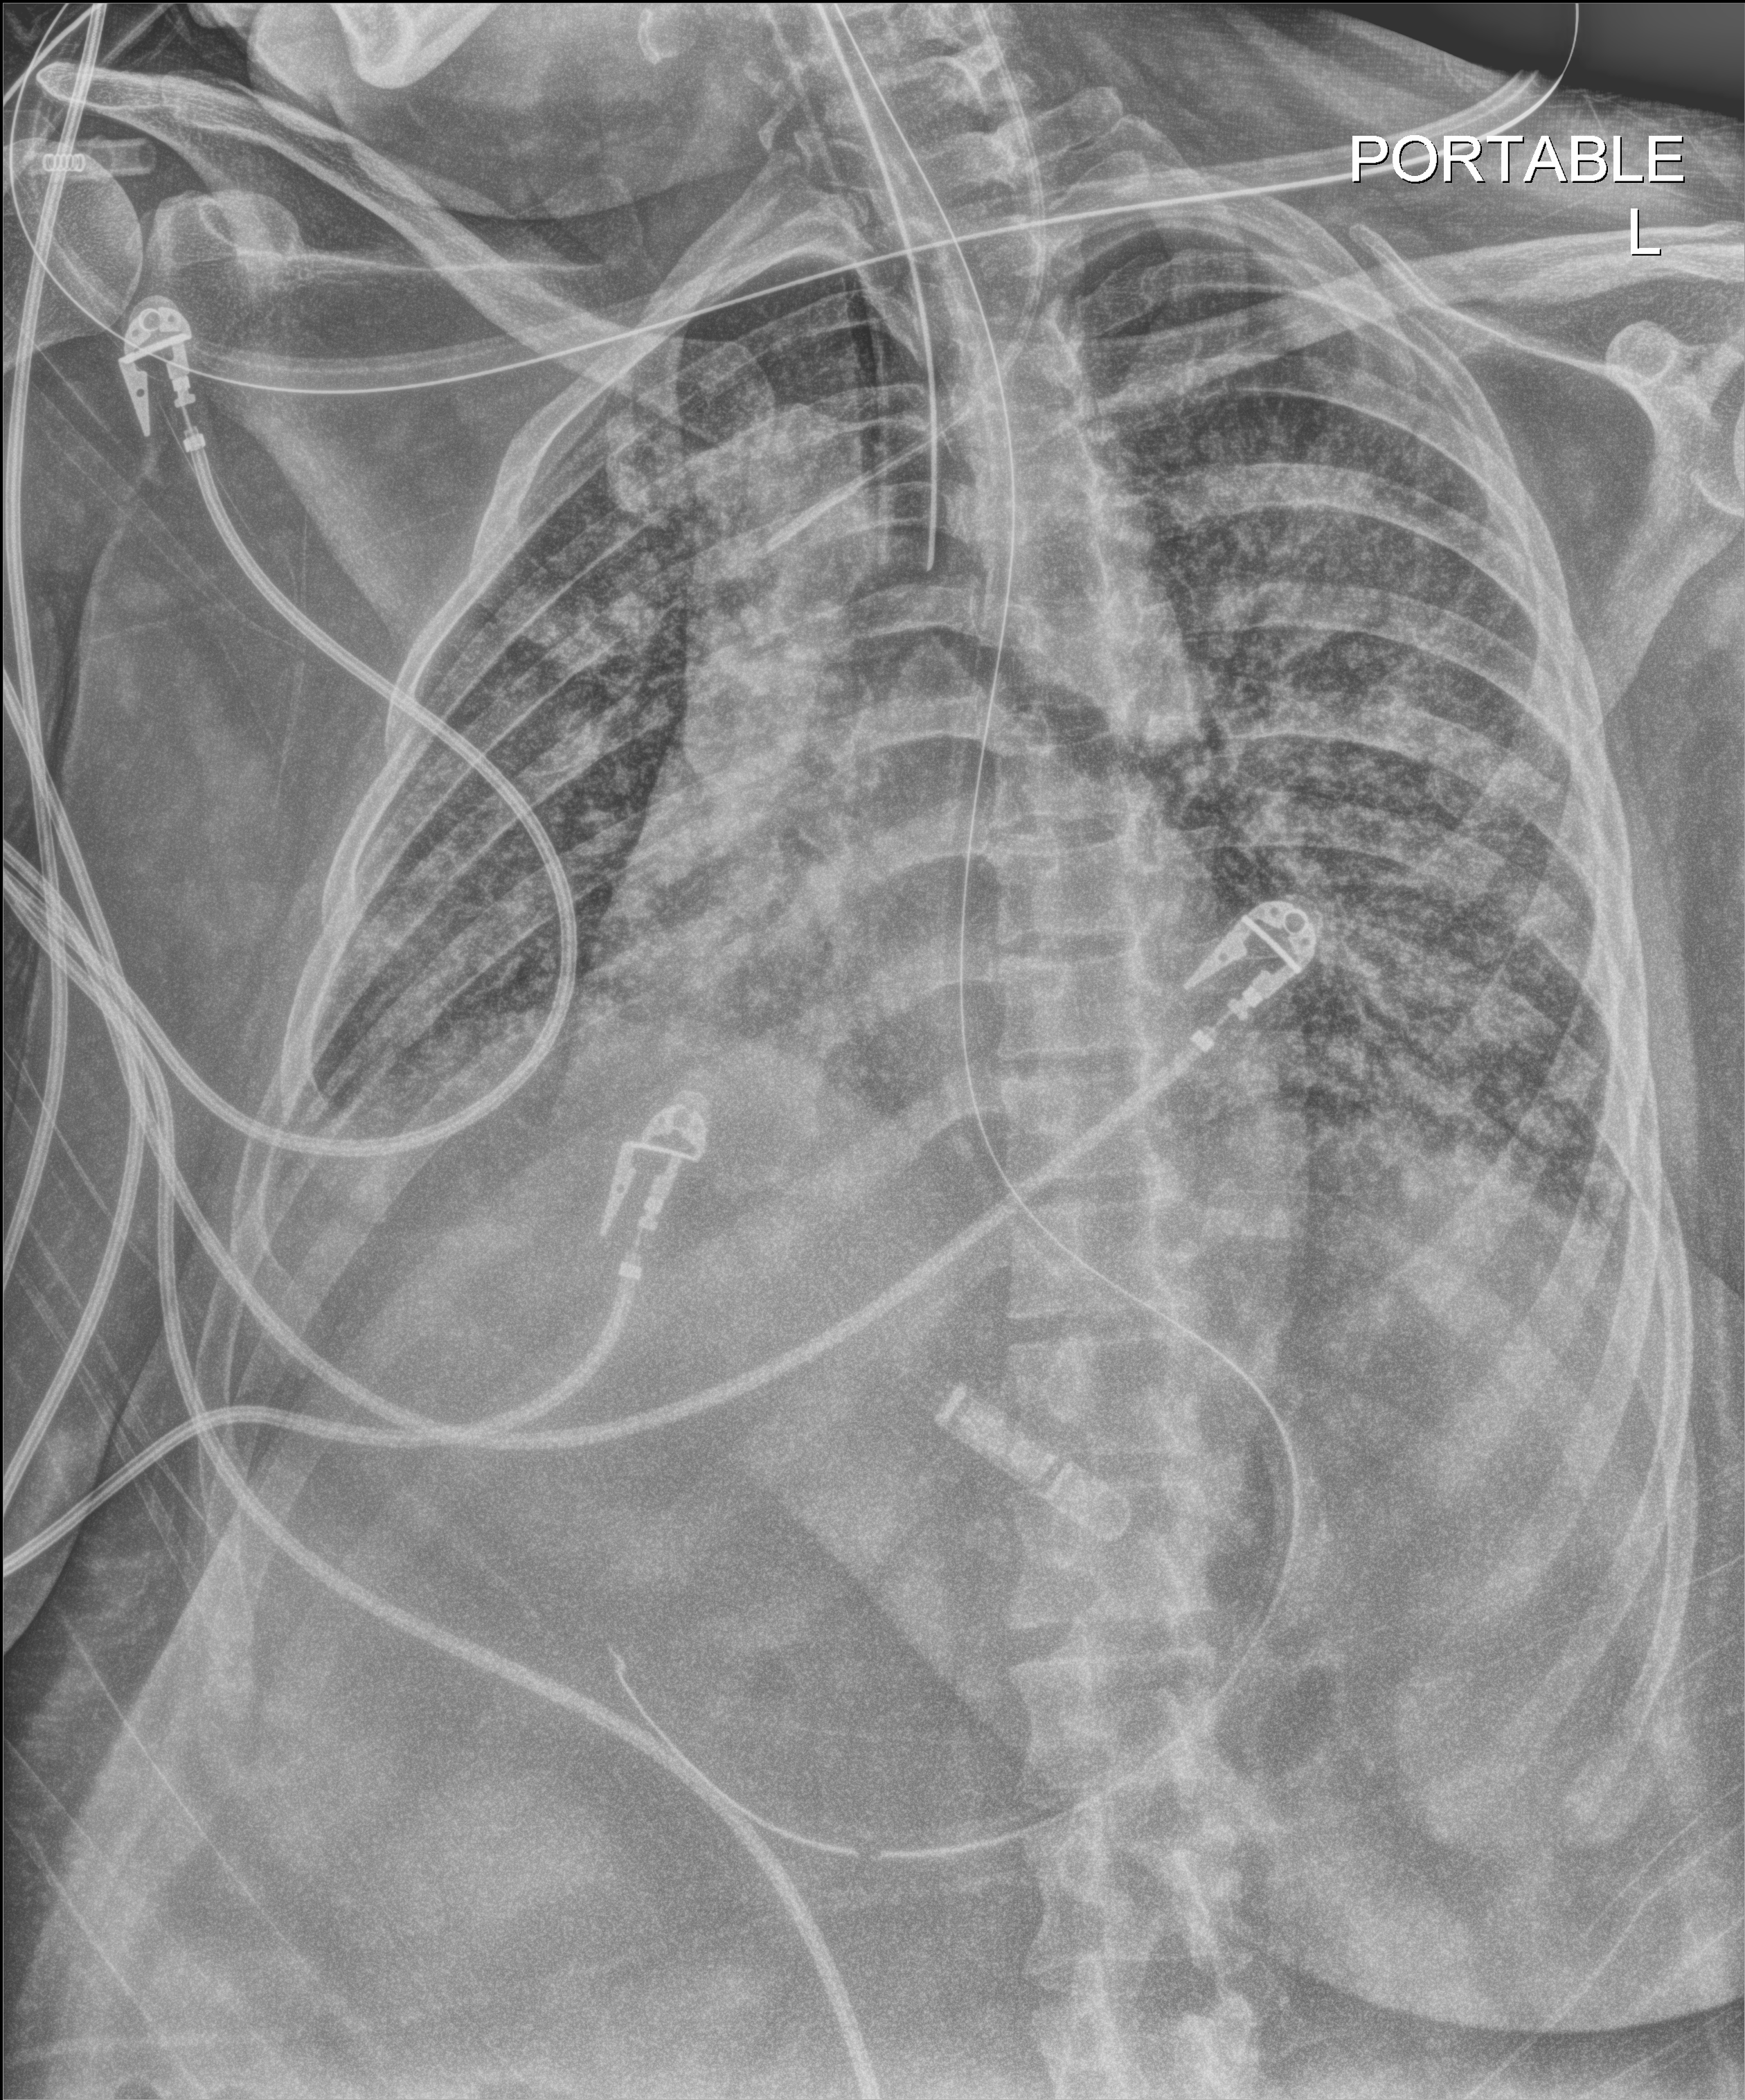
Chest radiograph (digital radiography), anteroposterior (AP) projection. Female patient hospitalised with COVID-19, age 18–59 years.
From the hospital-stay record, not from the radiograph (when in the stay this image was taken is not recorded):
- mechanically ventilated during this hospital stay: yes
- admitted to intensive care during this hospital stay: no